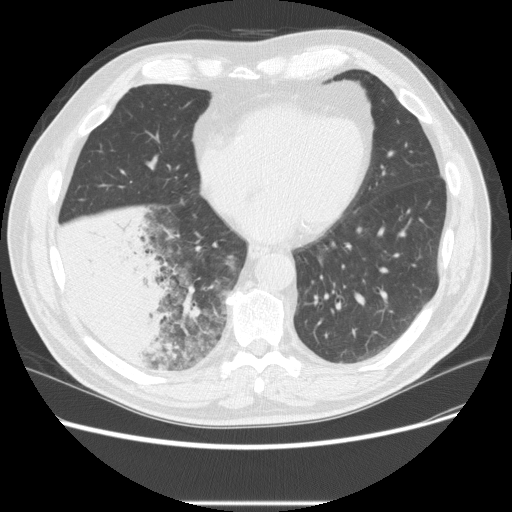
Low-dose screening chest CT, one axial slice; slice 81 of 233 in the series (ordered by position); 120 kVp; lung window (W 1500 / L -600 HU); 512 × 512 image matrix, field of view 380 × 380 mm.
Outlined on this slice (outlined manually by an expert reader):
- lesion 3 (tumor, lower lobe of right lung): bounding box [x1, y1, x2, y2] px = [55, 206, 176, 366]